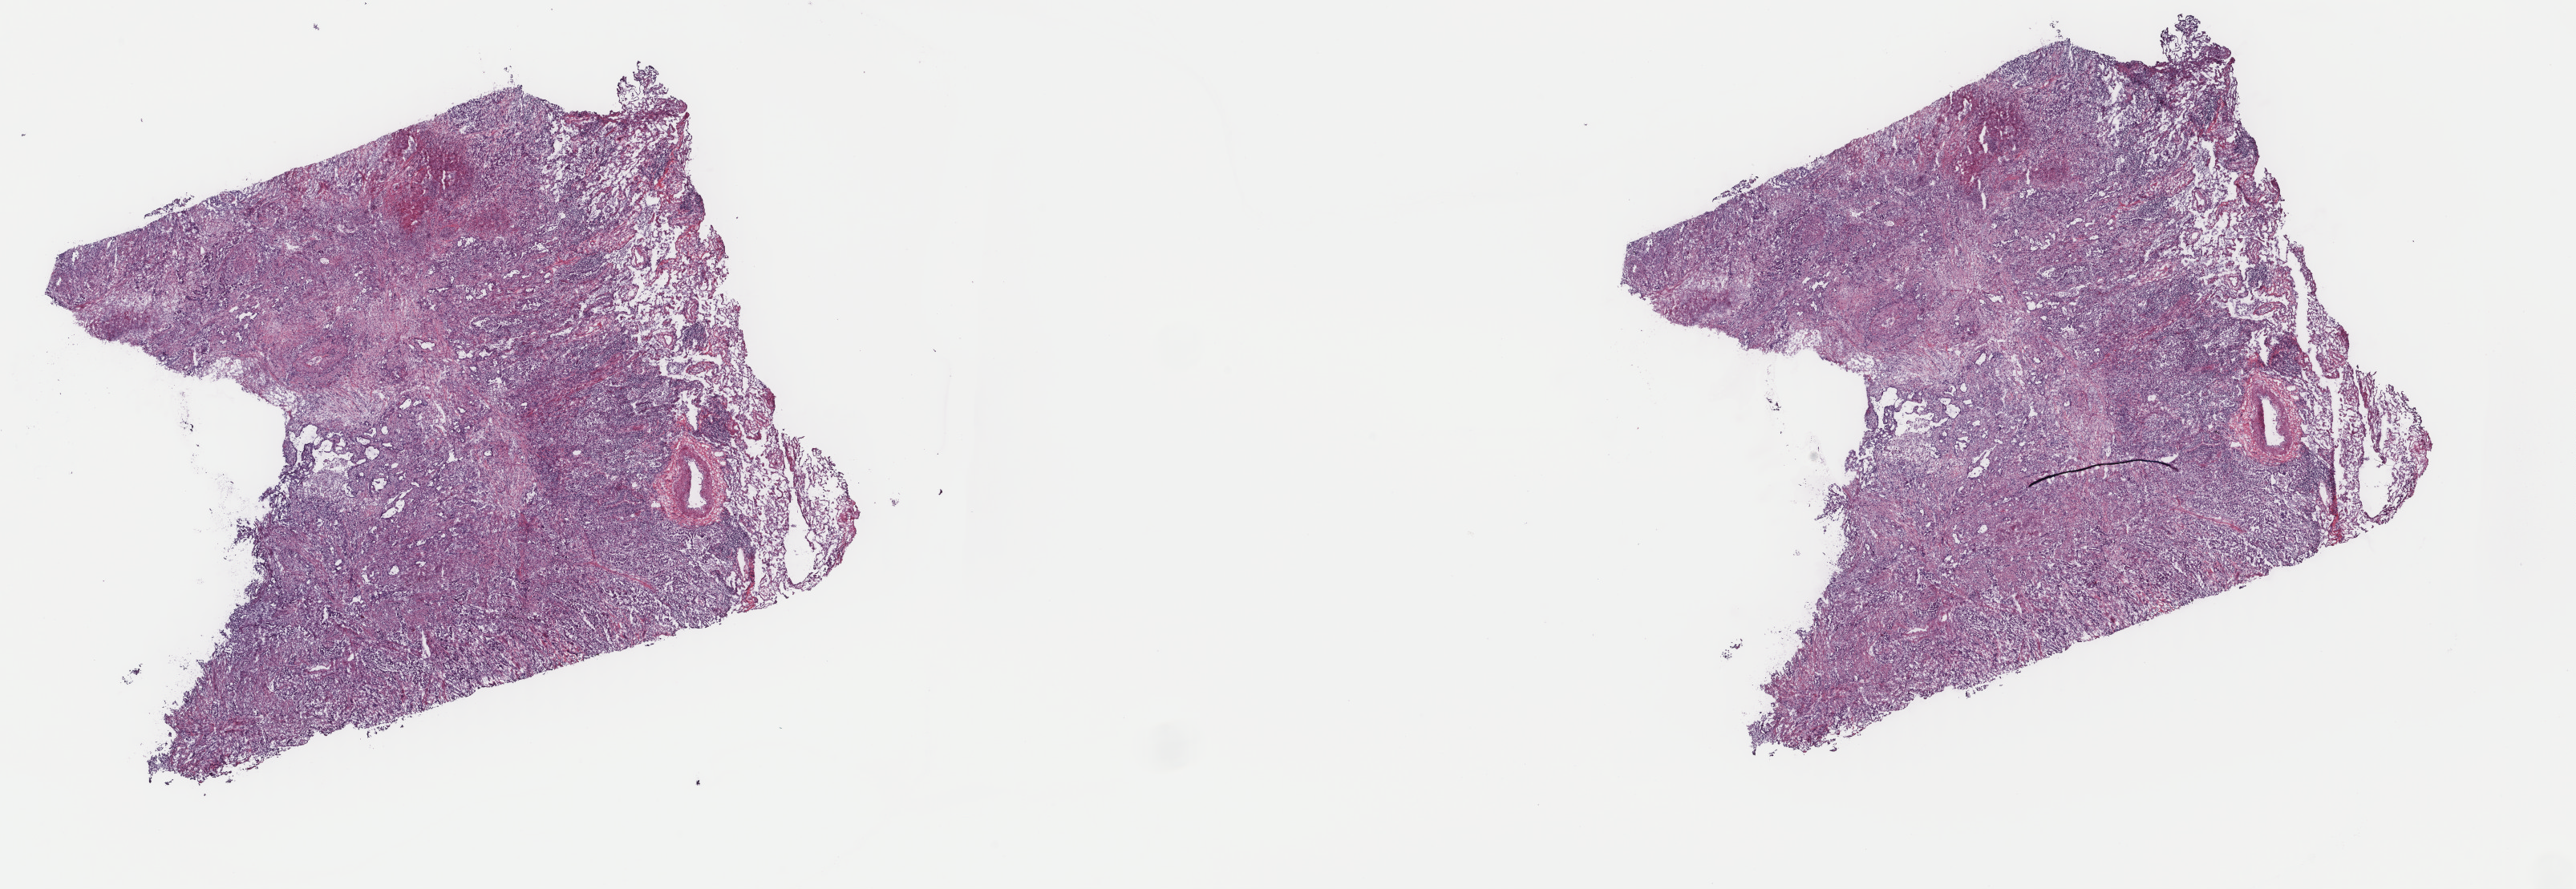
Whole-slide histology image, Hematoxylin and eosin (H&E) stained, whole scanned area (about 25.5 x 8.8 mm, slide scanned at 40x) shown as a low-resolution overview; frozen section from the top of the tissue portion; sample: primary tumour, lung. Male, age 77 years at initial diagnosis. Composition of this section per pathologist review: tumour cells 95%, tumour nuclei 68%, normal cells 5%, stromal cells 0%, necrosis 0%. Infiltration values recorded for this section: lymphocyte infiltration 0%, monocyte infiltration 0%, neutrophil infiltration 0%.
• pathologic diagnosis: Adenocarcinoma, NOS (middle lobe, lung)
• AJCC pathologic stage: IIIA (6th edition)